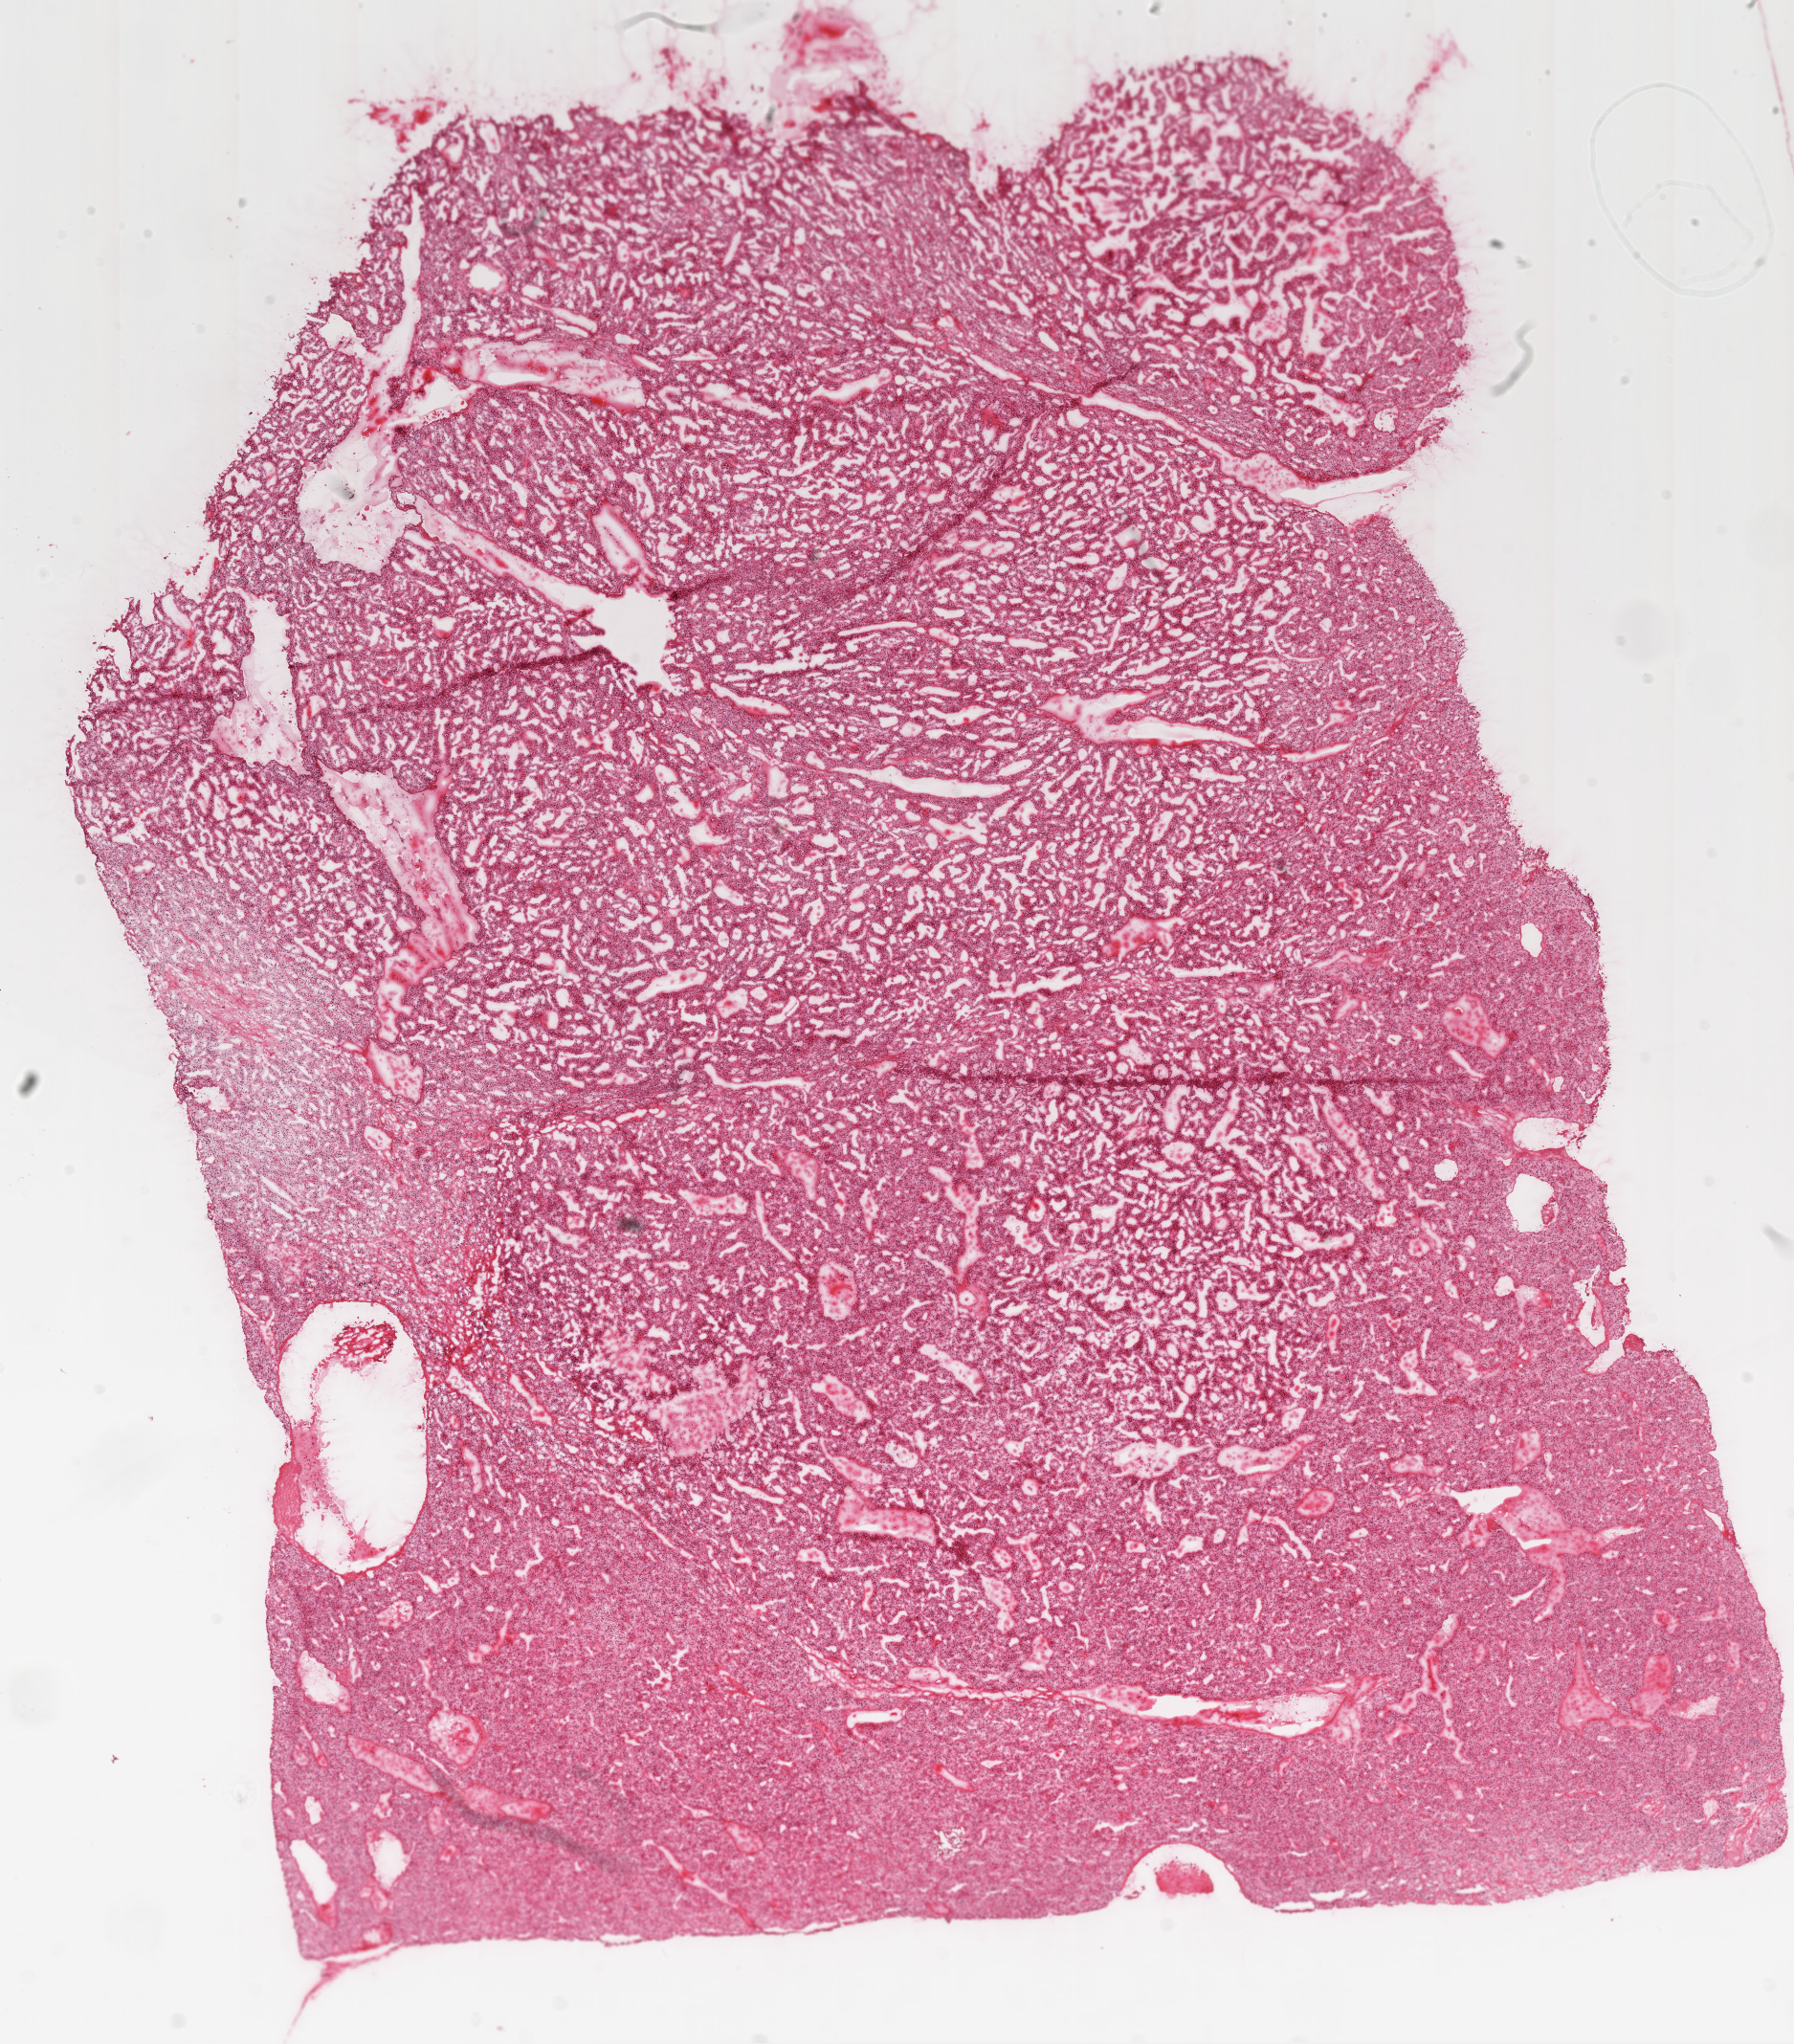
Digitized Hematoxylin and eosin (H&E) stained tissue section (whole slide), whole scanned area (about 15.0 x 17.1 mm, slide scanned at 20x) shown as a low-resolution overview. Frozen section. Kidney, primary tumour sample. Female, age 51 years at initial diagnosis. Histologic grade: G2 (moderately differentiated). Pathologist review of this section (percent, as recorded): tumour cells 95%, tumour nuclei 85%, normal cells 0%, stromal cells 5%, necrosis 0%.
Laterality: left. Histologic diagnosis: Clear cell adenocarcinoma, NOS. AJCC pathologic stage: III.